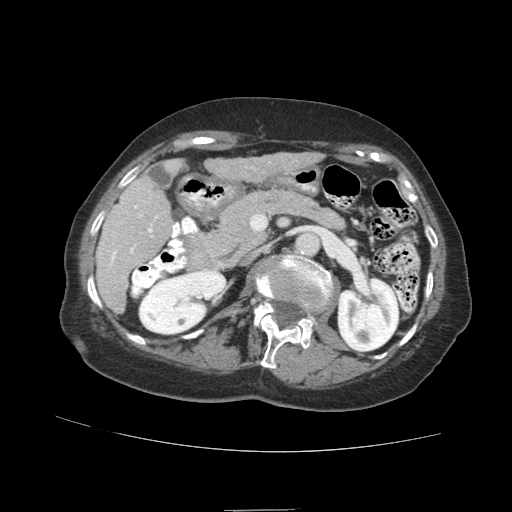
Contrast-enhanced abdominal CT (liver protocol), one axial slice. Slice 35 of 89 in the series (ordered by position). 140 kVp. Soft-tissue window (W 400 / L 40 HU). 2.5 mm slice thickness. 512 × 512 image matrix. Case-level facts recorded for this patient, not image findings: diagnosis: hepatocellular carcinoma (patient treated with transarterial chemoembolisation; whether this scan precedes or follows treatment is not stated here); TNM stage (as recorded): Stage-II; Child-Pugh class: A; tumour size: 4 cm.
Structures marked on this image (semi-automatic segmentation, software-assisted and operator-edited):
- liver parenchyma outside the tumour (the mass and vessels are separate outlines, so this box may not span the whole liver): box from (x=96, y=152) to (x=322, y=312) px
- liver vessels: (x=109, y=205)–(x=158, y=266)